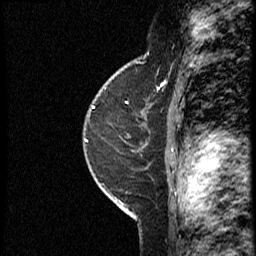
Breast MRI (dynamic contrast-enhanced), one sagittal slice; slice 26 of 40 in the series (ordered by position); dynamic contrast-enhanced study with each time point stored as its own series, time point 2 of 4 at this slice position (early post-contrast, ordered by acquisition time); 1.5 T; TE 4.2 ms, TR 18.8 ms; 3 mm slice thickness; 256 × 256 image matrix, field of view 200 × 200 mm. Female patient. From the clinical record (not read from this slice): setting: breast cancer imaged before/during neoadjuvant chemotherapy; receptor status: HER2-positive.
Structures marked on this image (semi-automatic segmentation, software-assisted and operator-edited):
- analysis volume of interest (the breast-tissue region the enhancement analysis was run in; not a lesion): box from (x=91, y=79) to (x=169, y=152) px
- tumour enhancement mask (voxels above the 100 % enhancement threshold inside the analysis volume of interest): (x=93, y=106)–(x=96, y=109)